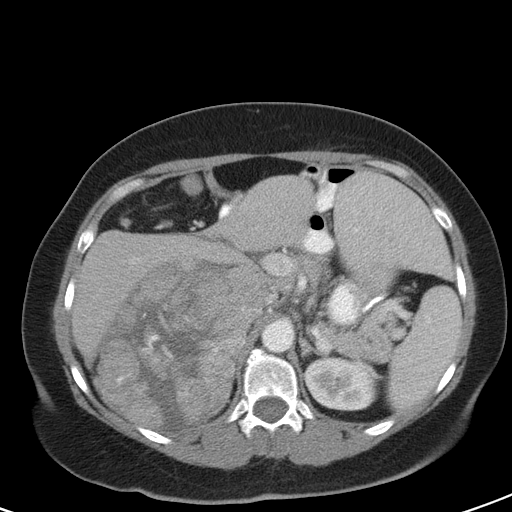
Contrast-enhanced abdominal CT, one axial slice. Position 72 of 126 along the scan axis. Intravenous contrast given. Soft-tissue window (W 400 / L 40 HU). 512 × 512 image matrix, field of view 356 × 356 mm. Patient: female, 51 years. From the clinical record (not read from this slice): diagnosis: adrenocortical carcinoma; tumour side: right adrenal; tumour size at pathology: 17 cm; Ki-67 index: 12 %; stage (as recorded): 2.
Structures marked on this image (semi-automatic segmentation, software-assisted and operator-edited):
- mass: bounding box (x1, y1, x2, y2) in pixels: (97, 261, 262, 426)